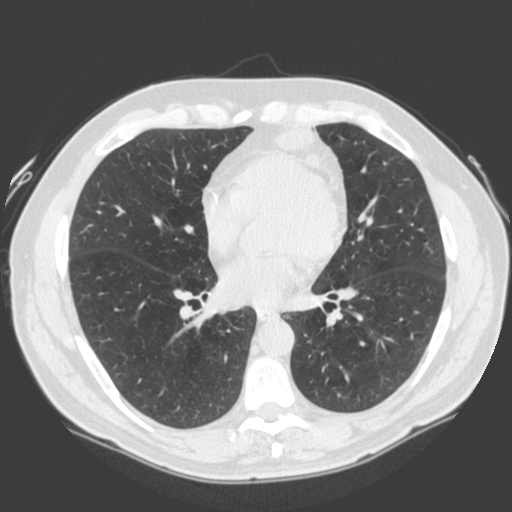
Low-dose screening chest CT, one axial slice; slice 87 of 185 in the series (ordered by position); 120 kVp; lung window (W 1500 / L -600 HU); 512 × 512 image matrix.
Structures marked on this image (expert manual segmentation):
- lesion 1 (tumor, lower lobe of left lung): bounding box <275,128,339,176> (left, top, right, bottom; pixels)